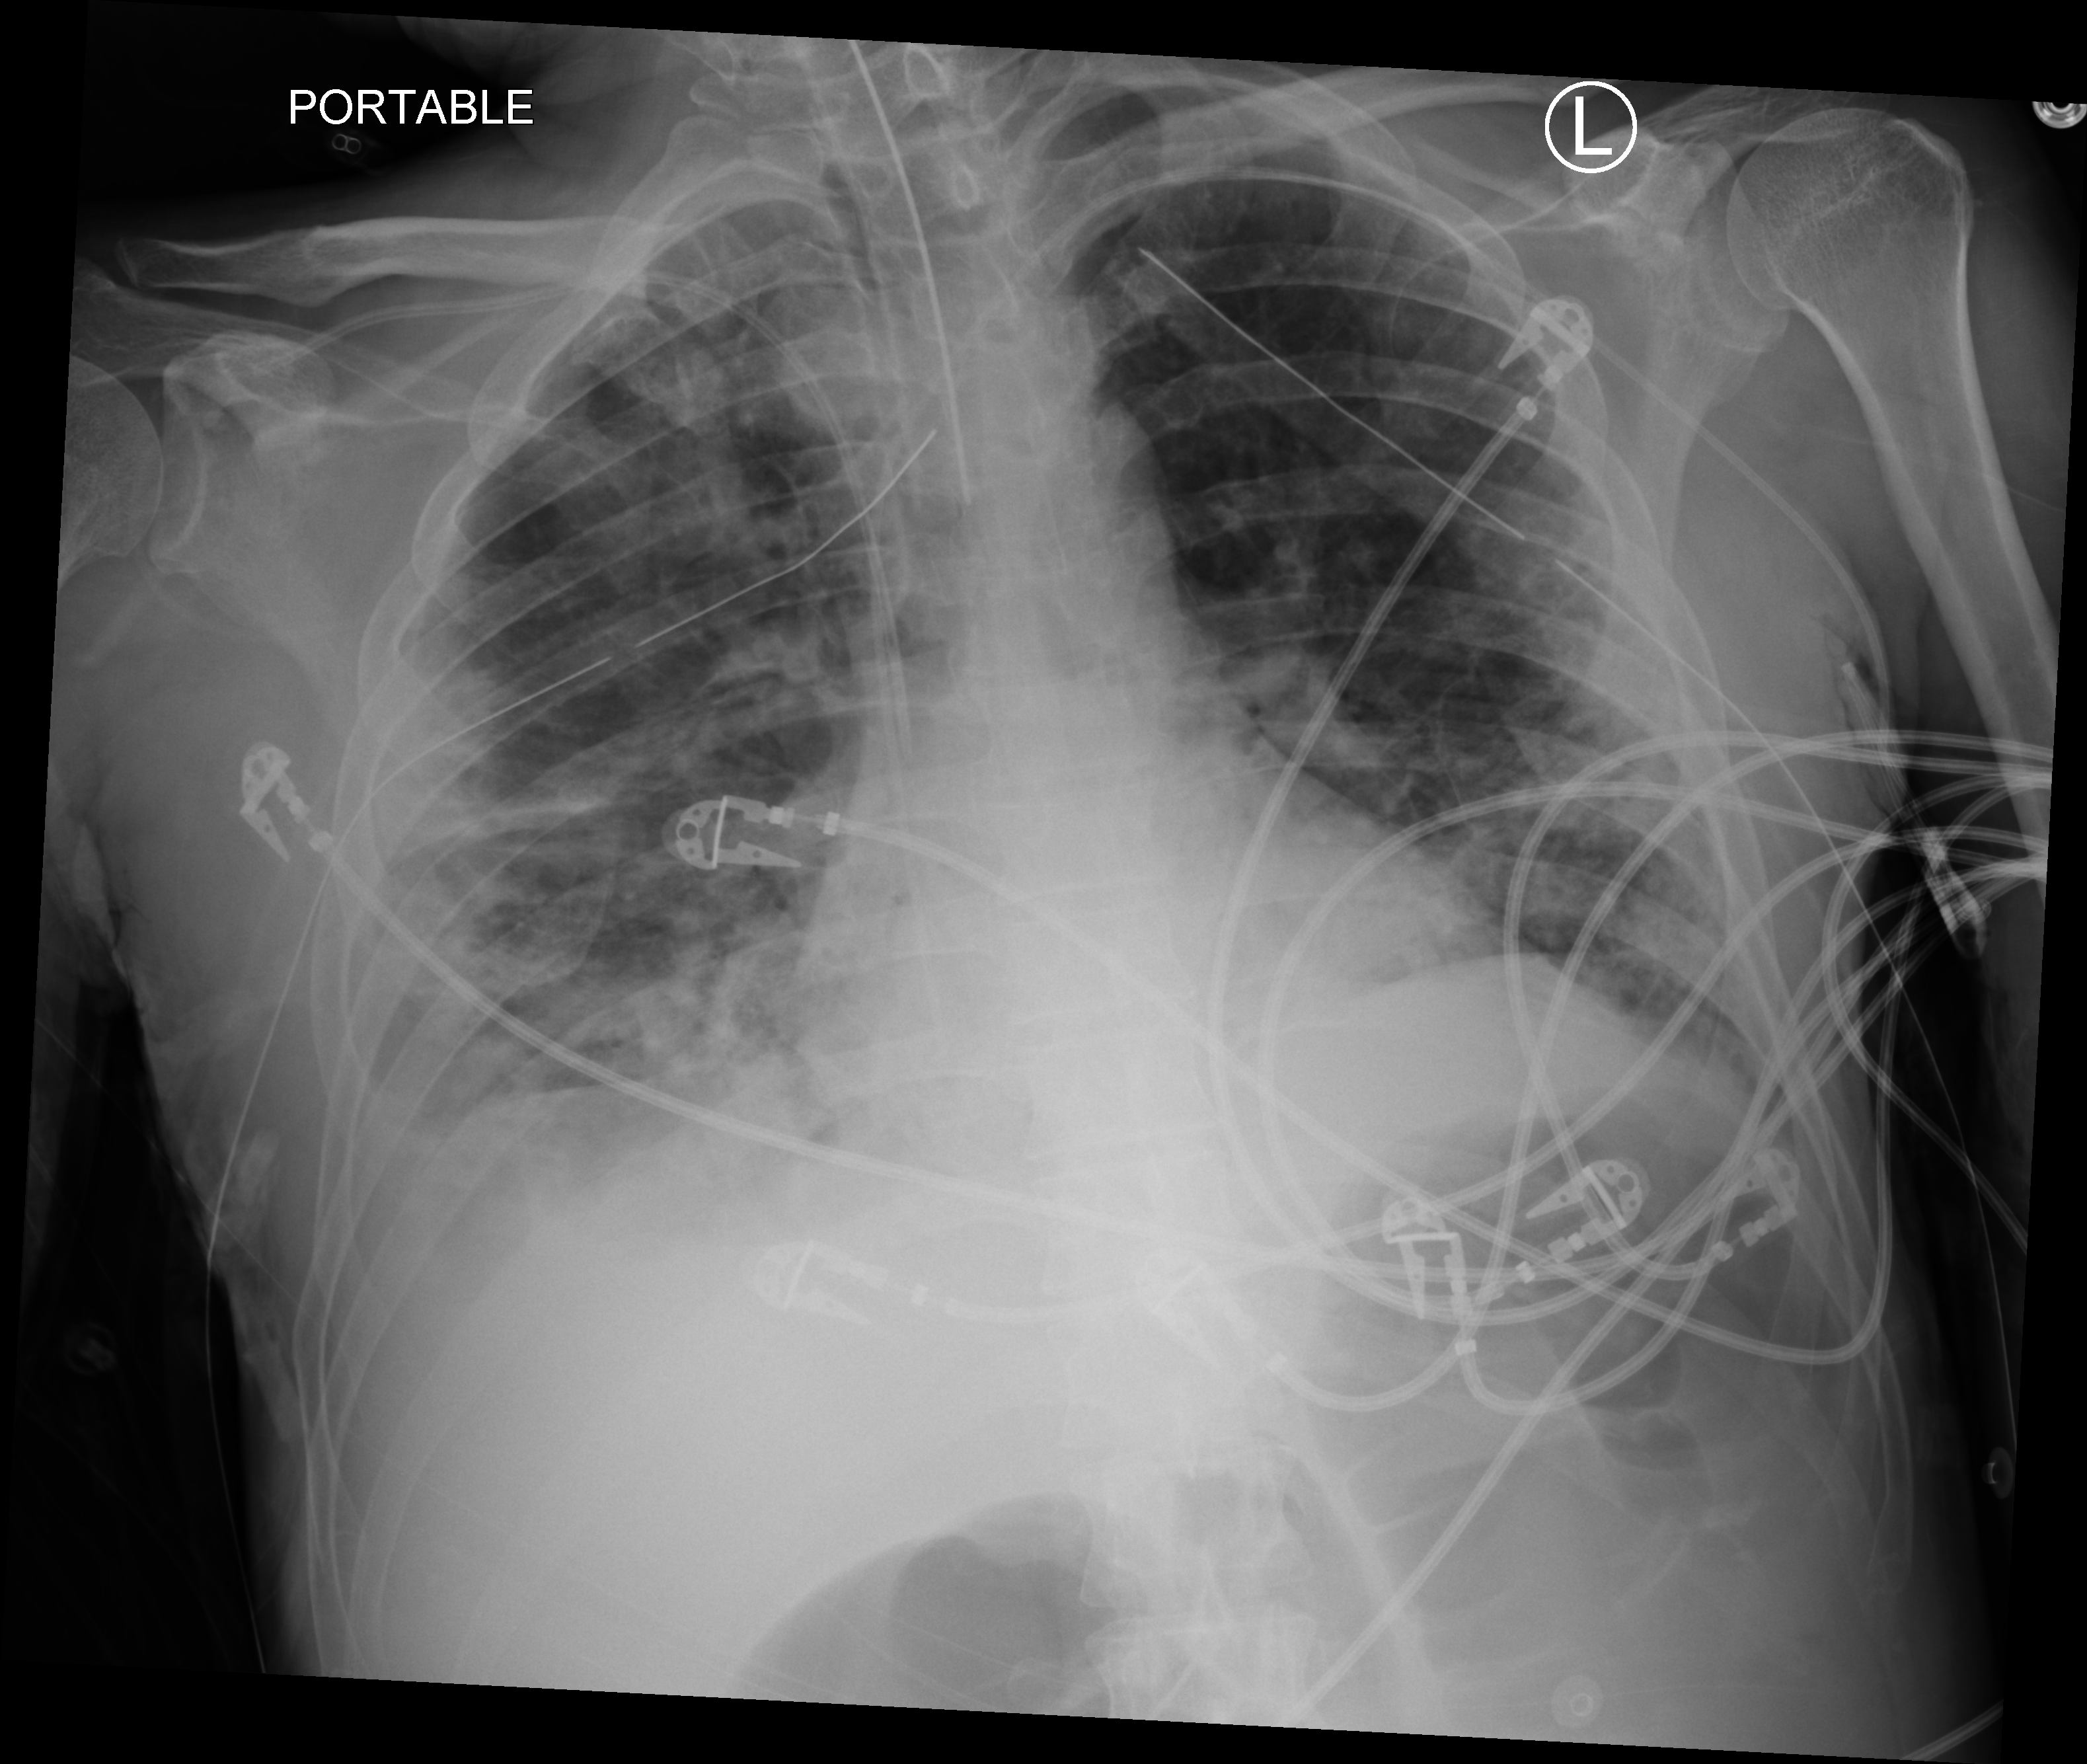
Portable chest radiograph, anteroposterior (AP) projection. Male patient hospitalised with COVID-19, age 18–59 years.
From the hospital-stay record, not from the radiograph (when in the stay this image was taken is not recorded): admitted to intensive care during this hospital stay: yes.